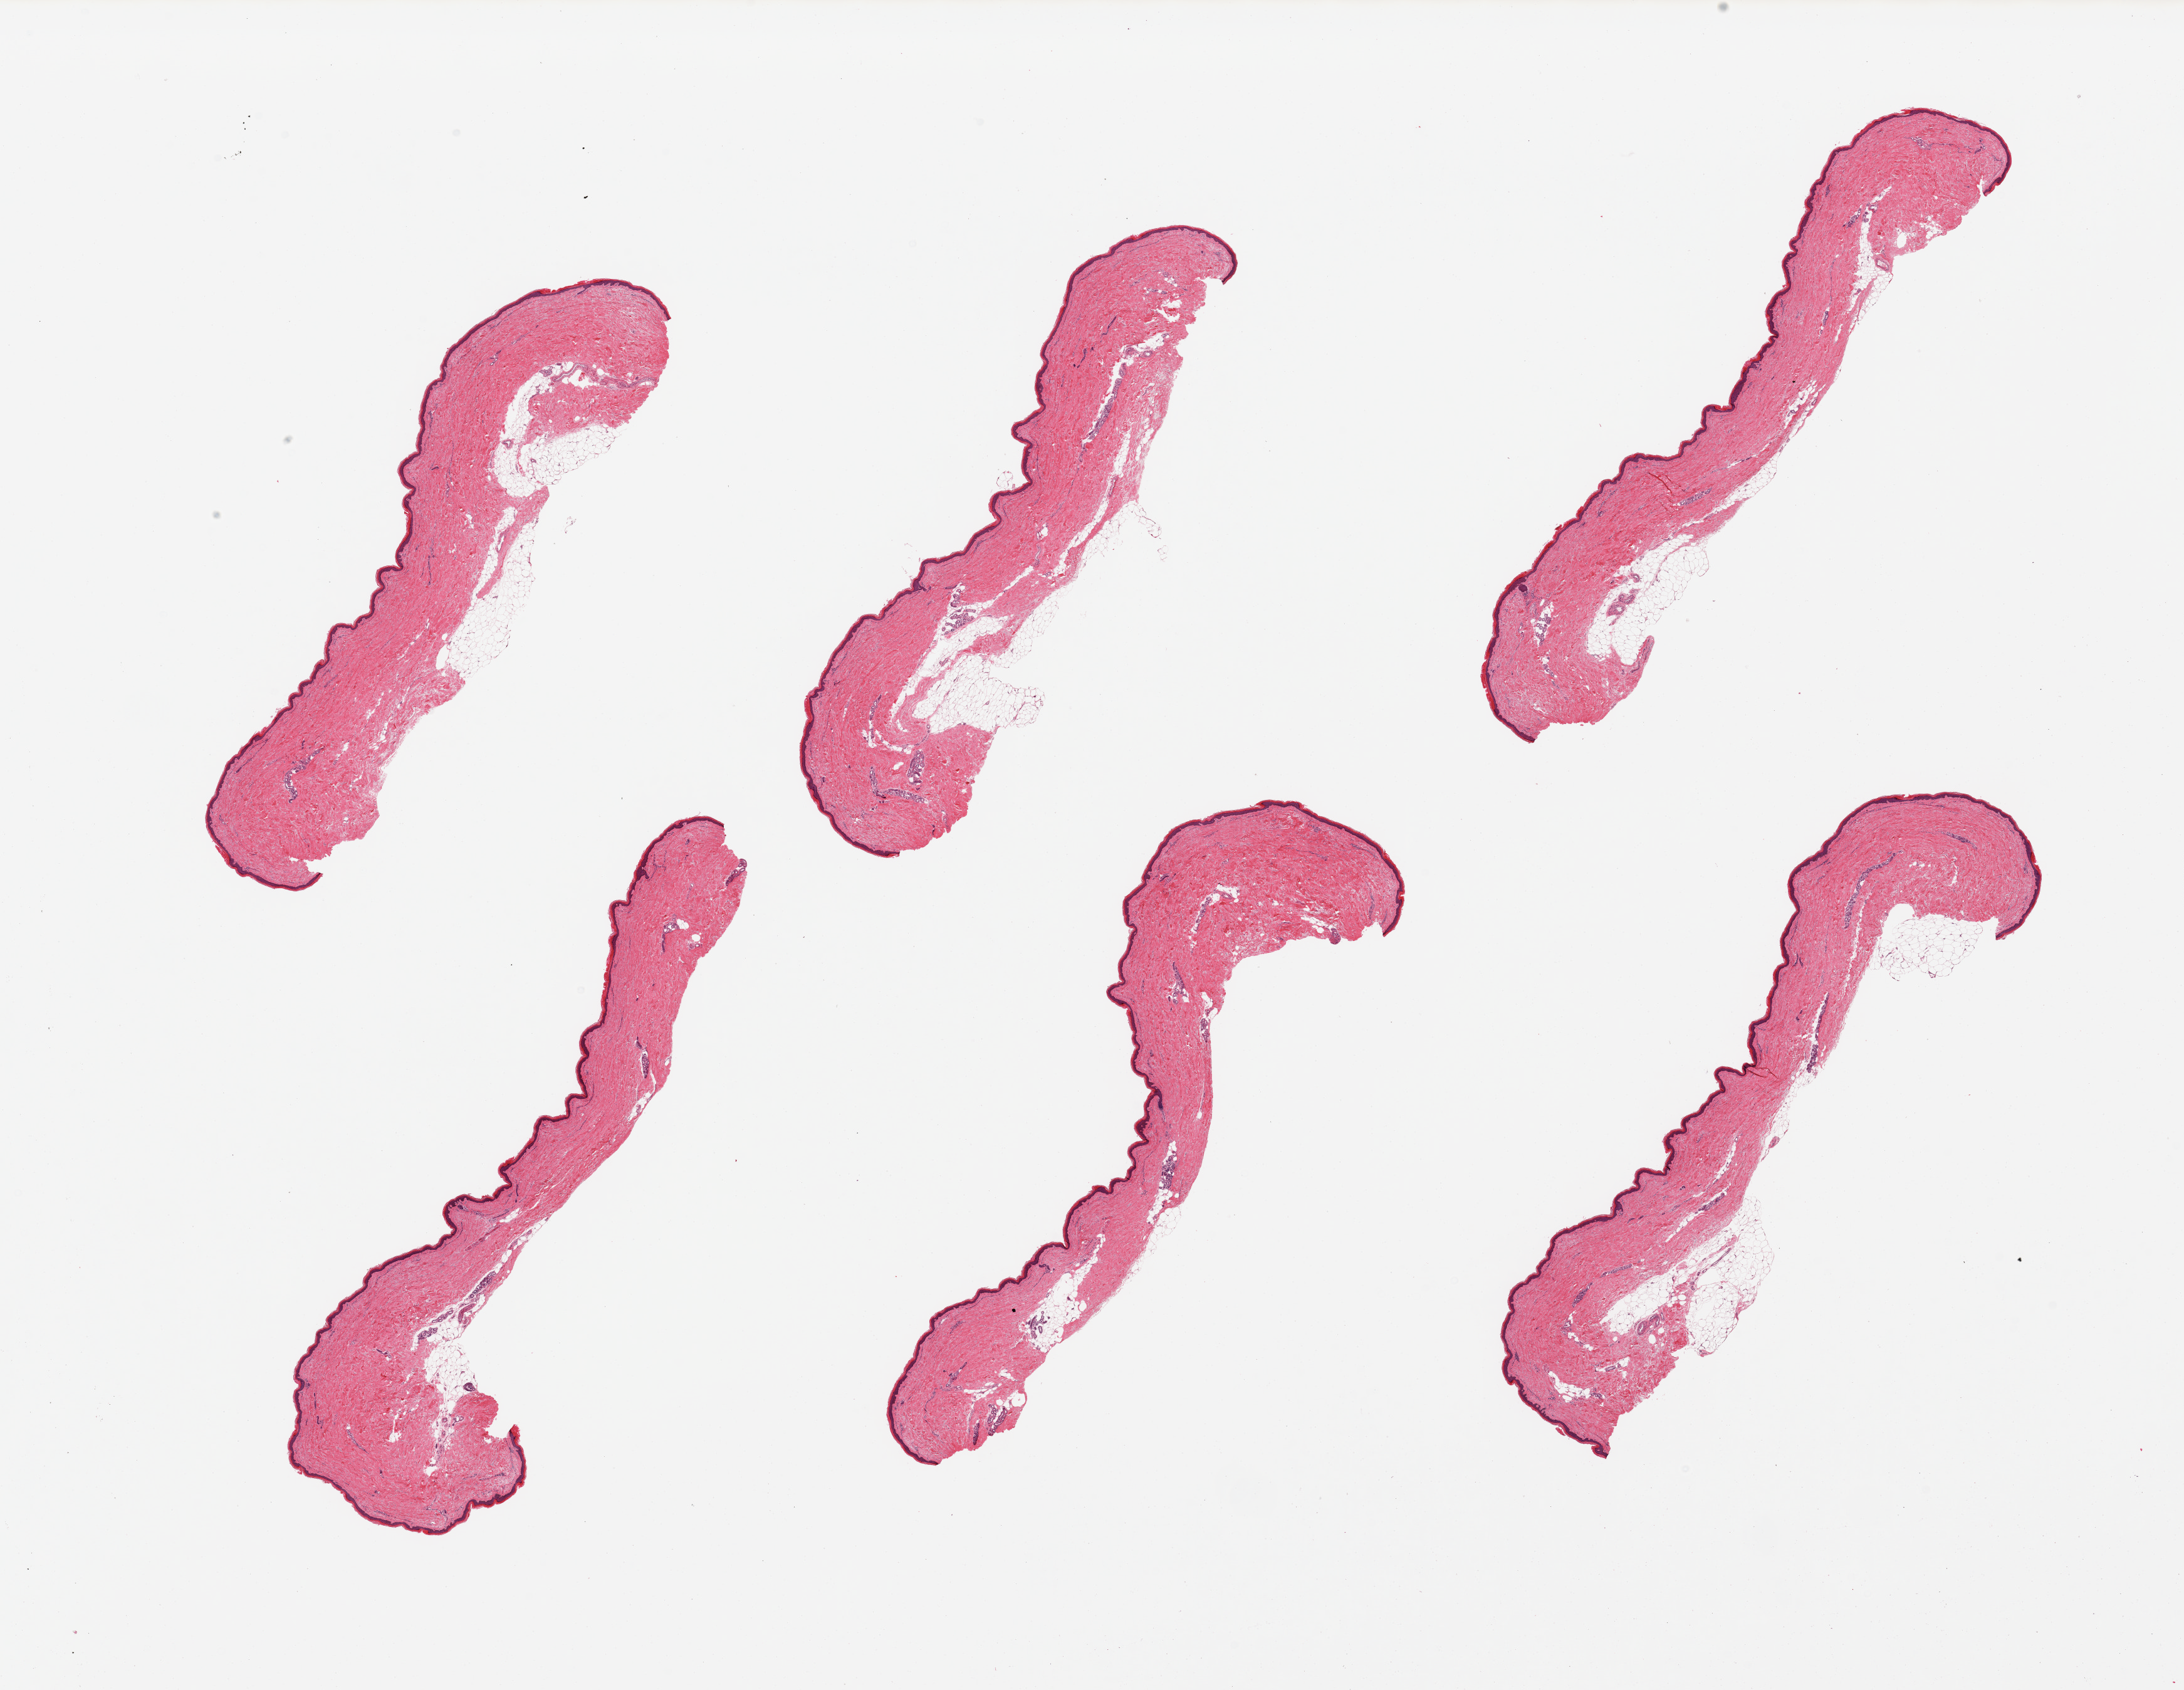
H&E whole-slide image — low-resolution overview of the scanned area, about 27.6 x 21.3 mm (slide scanned at 20x); PAXgene-fixed paraffin-embedded (PFPE) section; target tissue: skin of lower leg; donor tissue sample. Donor: female.
Review note (as recorded): 6 pieces, 5-10% attached and internal adipose tissue, squamous epithelium measures 30-40 microns in thickness.